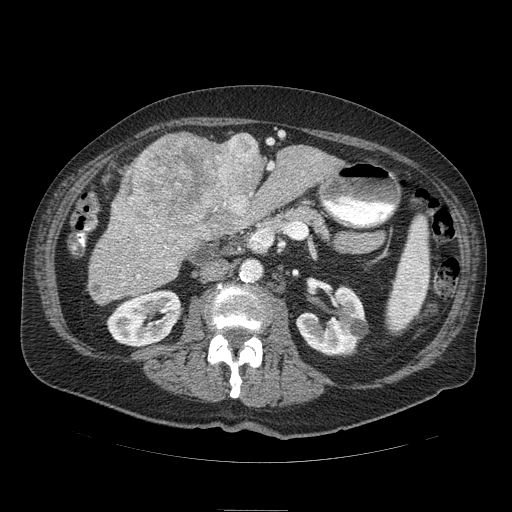
Contrast-enhanced abdominal CT (liver protocol), one axial slice; position 32 of 103 along the scan axis; soft-tissue window (W 400 / L 40 HU); 2.5 mm slice thickness; 512 × 512 image matrix. Case-level facts recorded for this patient, not image findings: diagnosis: hepatocellular carcinoma (patient treated with transarterial chemoembolisation; whether this scan precedes or follows treatment is not stated here); TNM stage (as recorded): Stage-IIIA; Child-Pugh class: B; tumour differentiation: well differentiated; tumour nodularity: multinodular.
Outlined on this slice (semi-automatically segmented with operator editing):
- liver parenchyma outside the tumour (the mass and vessels are separate outlines, so this box may not span the whole liver): bounding box (x1, y1, x2, y2) in pixels: (92, 132, 341, 292)
- mass: (114, 132, 264, 254)
- liver vessels: (123, 163, 274, 285)